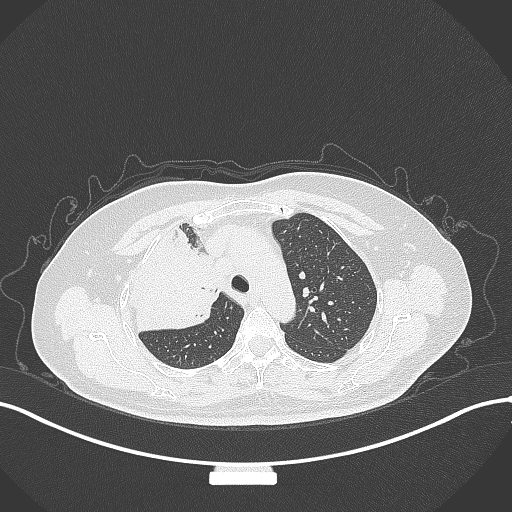
Chest CT, one axial slice. Position 229 of 309 along the scan axis. 120 kVp. Lung window (W 1500 / L -600 HU). 512 × 512 image matrix, field of view 400 × 400 mm. Patient: female, 60 years. Case-level facts recorded for this patient, not image findings: clinical TNM (as recorded): T3 N1 M1.
Outlined on this slice (bounding box drawn by a radiologist):
- lung tumour (recorded histology: adenocarcinoma): bounding box (x1, y1, x2, y2) in pixels: (128, 225, 224, 339)